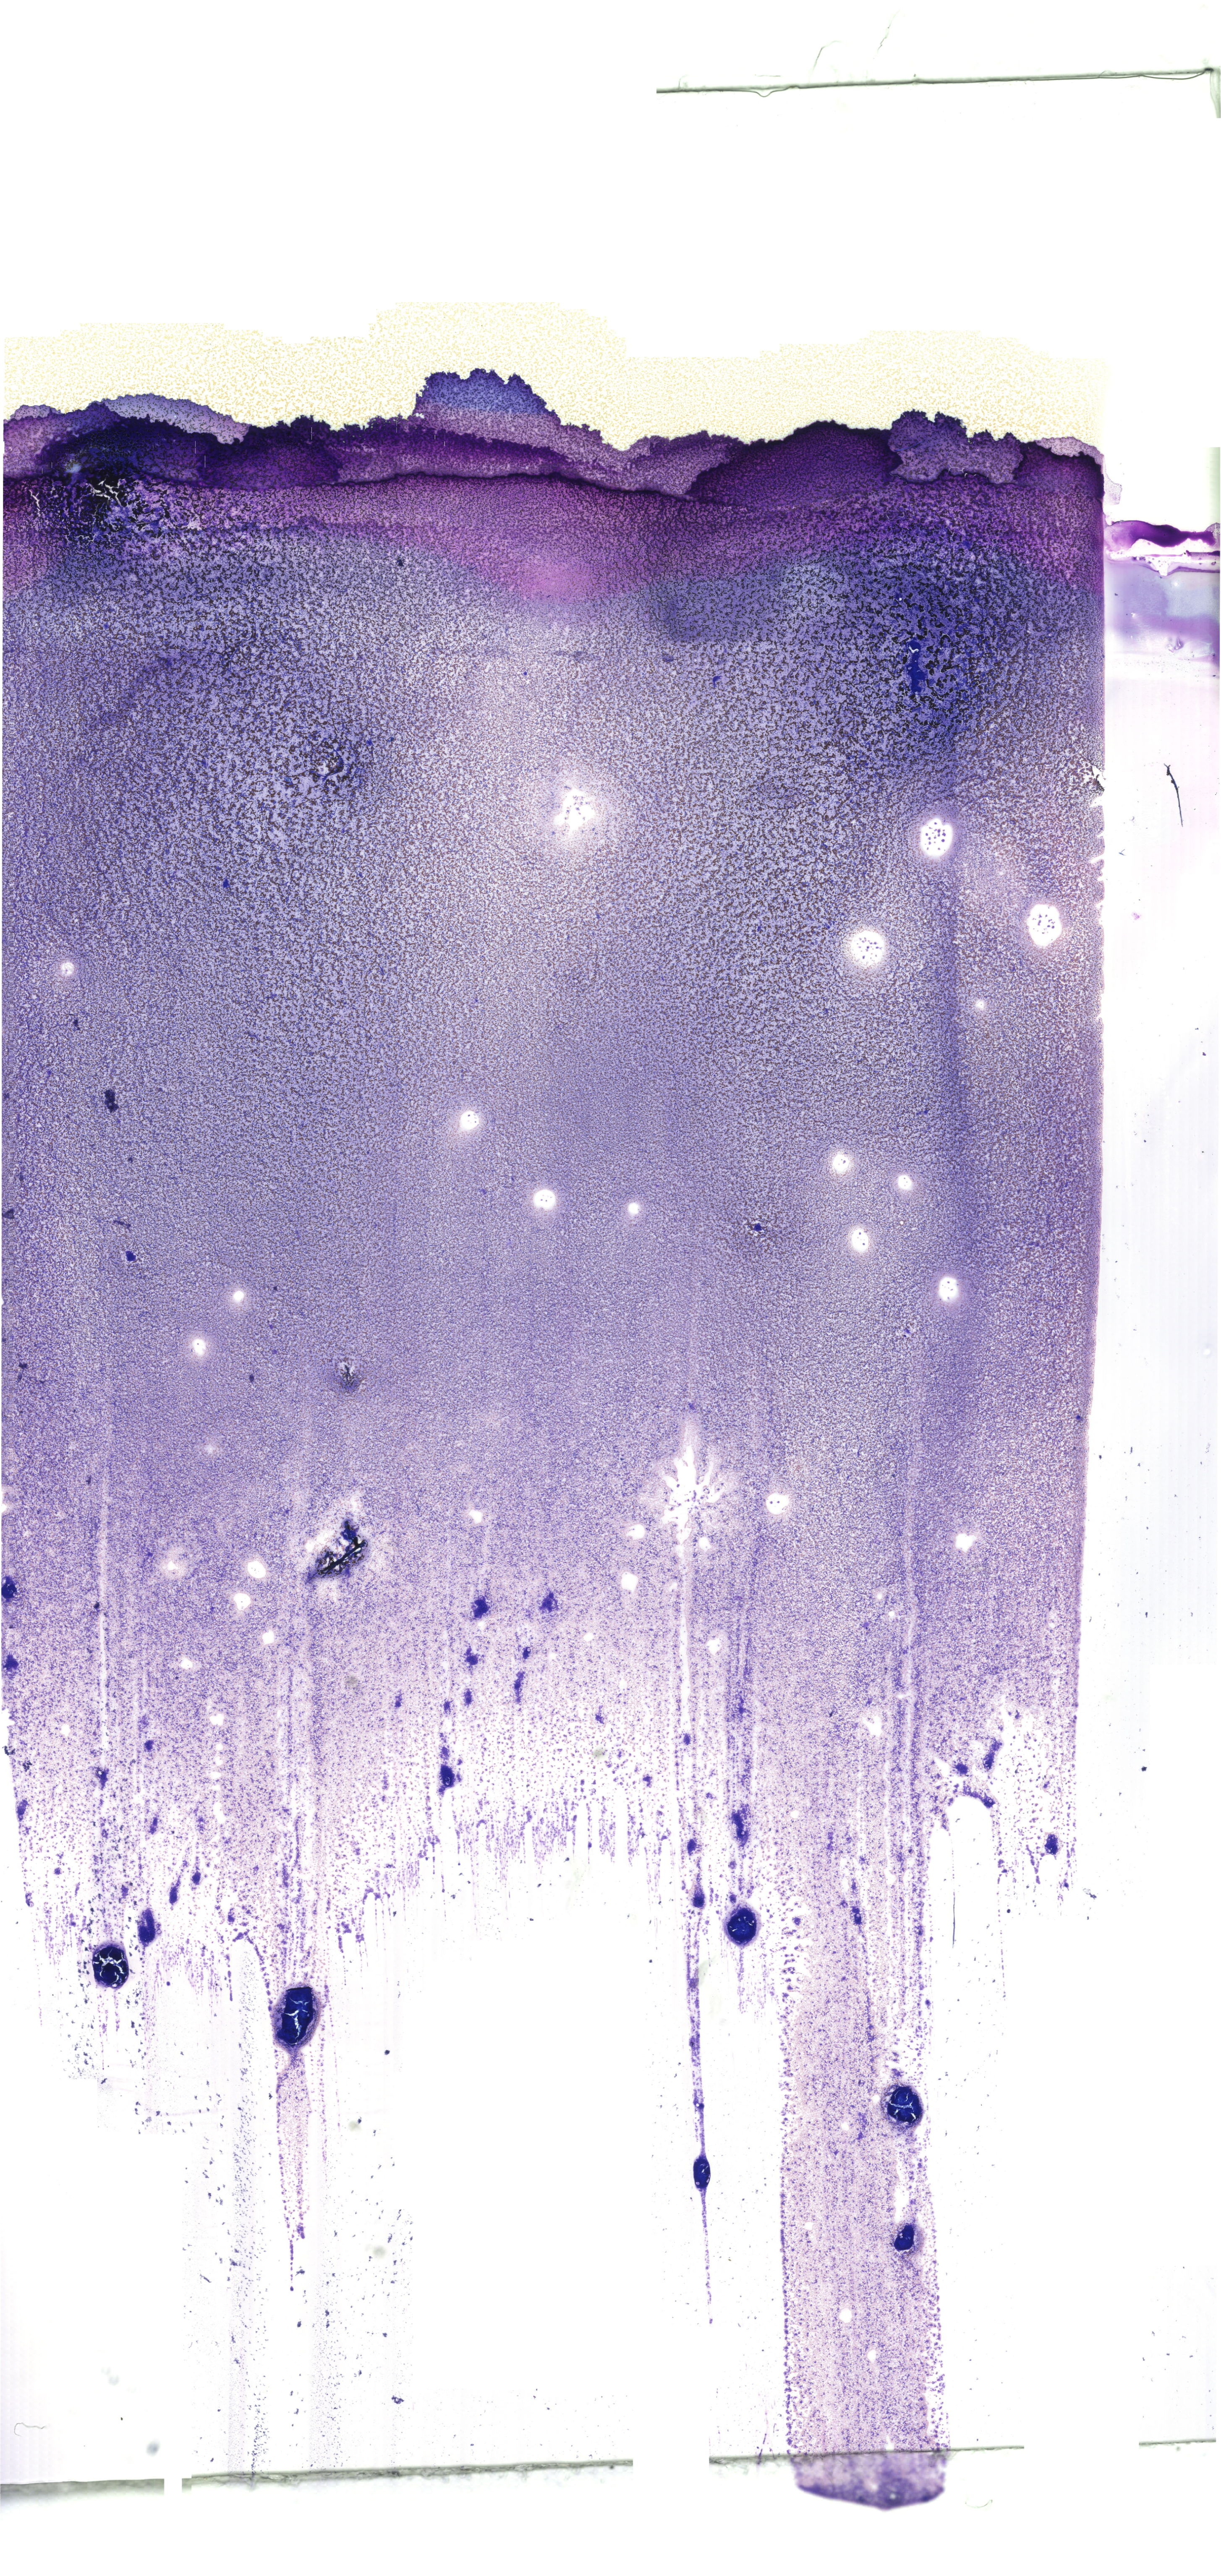
May-Grünwald-Giemsa (MGG)-stained marrow aspirate smear (whole slide), shown as a low-resolution overview of the whole scanned area (about 20.6 x 43.5 mm). Female patient.
Diagnosis: Acute Myeloid Leukemia with Maturation.